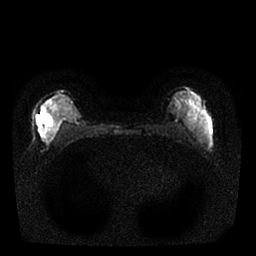
Breast MRI, one axial slice. Position 9 of 25 along the scan axis. Diffusion-weighted series; image 2 of 4 stored at this slice position (different b-values; order by instance number). 1.5 T. 4 mm slice thickness. 256 × 256 image matrix, field of view 310 × 310 mm. Female patient.
Annotated regions visible in this slice (expert manual segmentation):
- tumour on diffusion-weighted imaging: bounding box <39,113,57,141> (left, top, right, bottom; pixels)